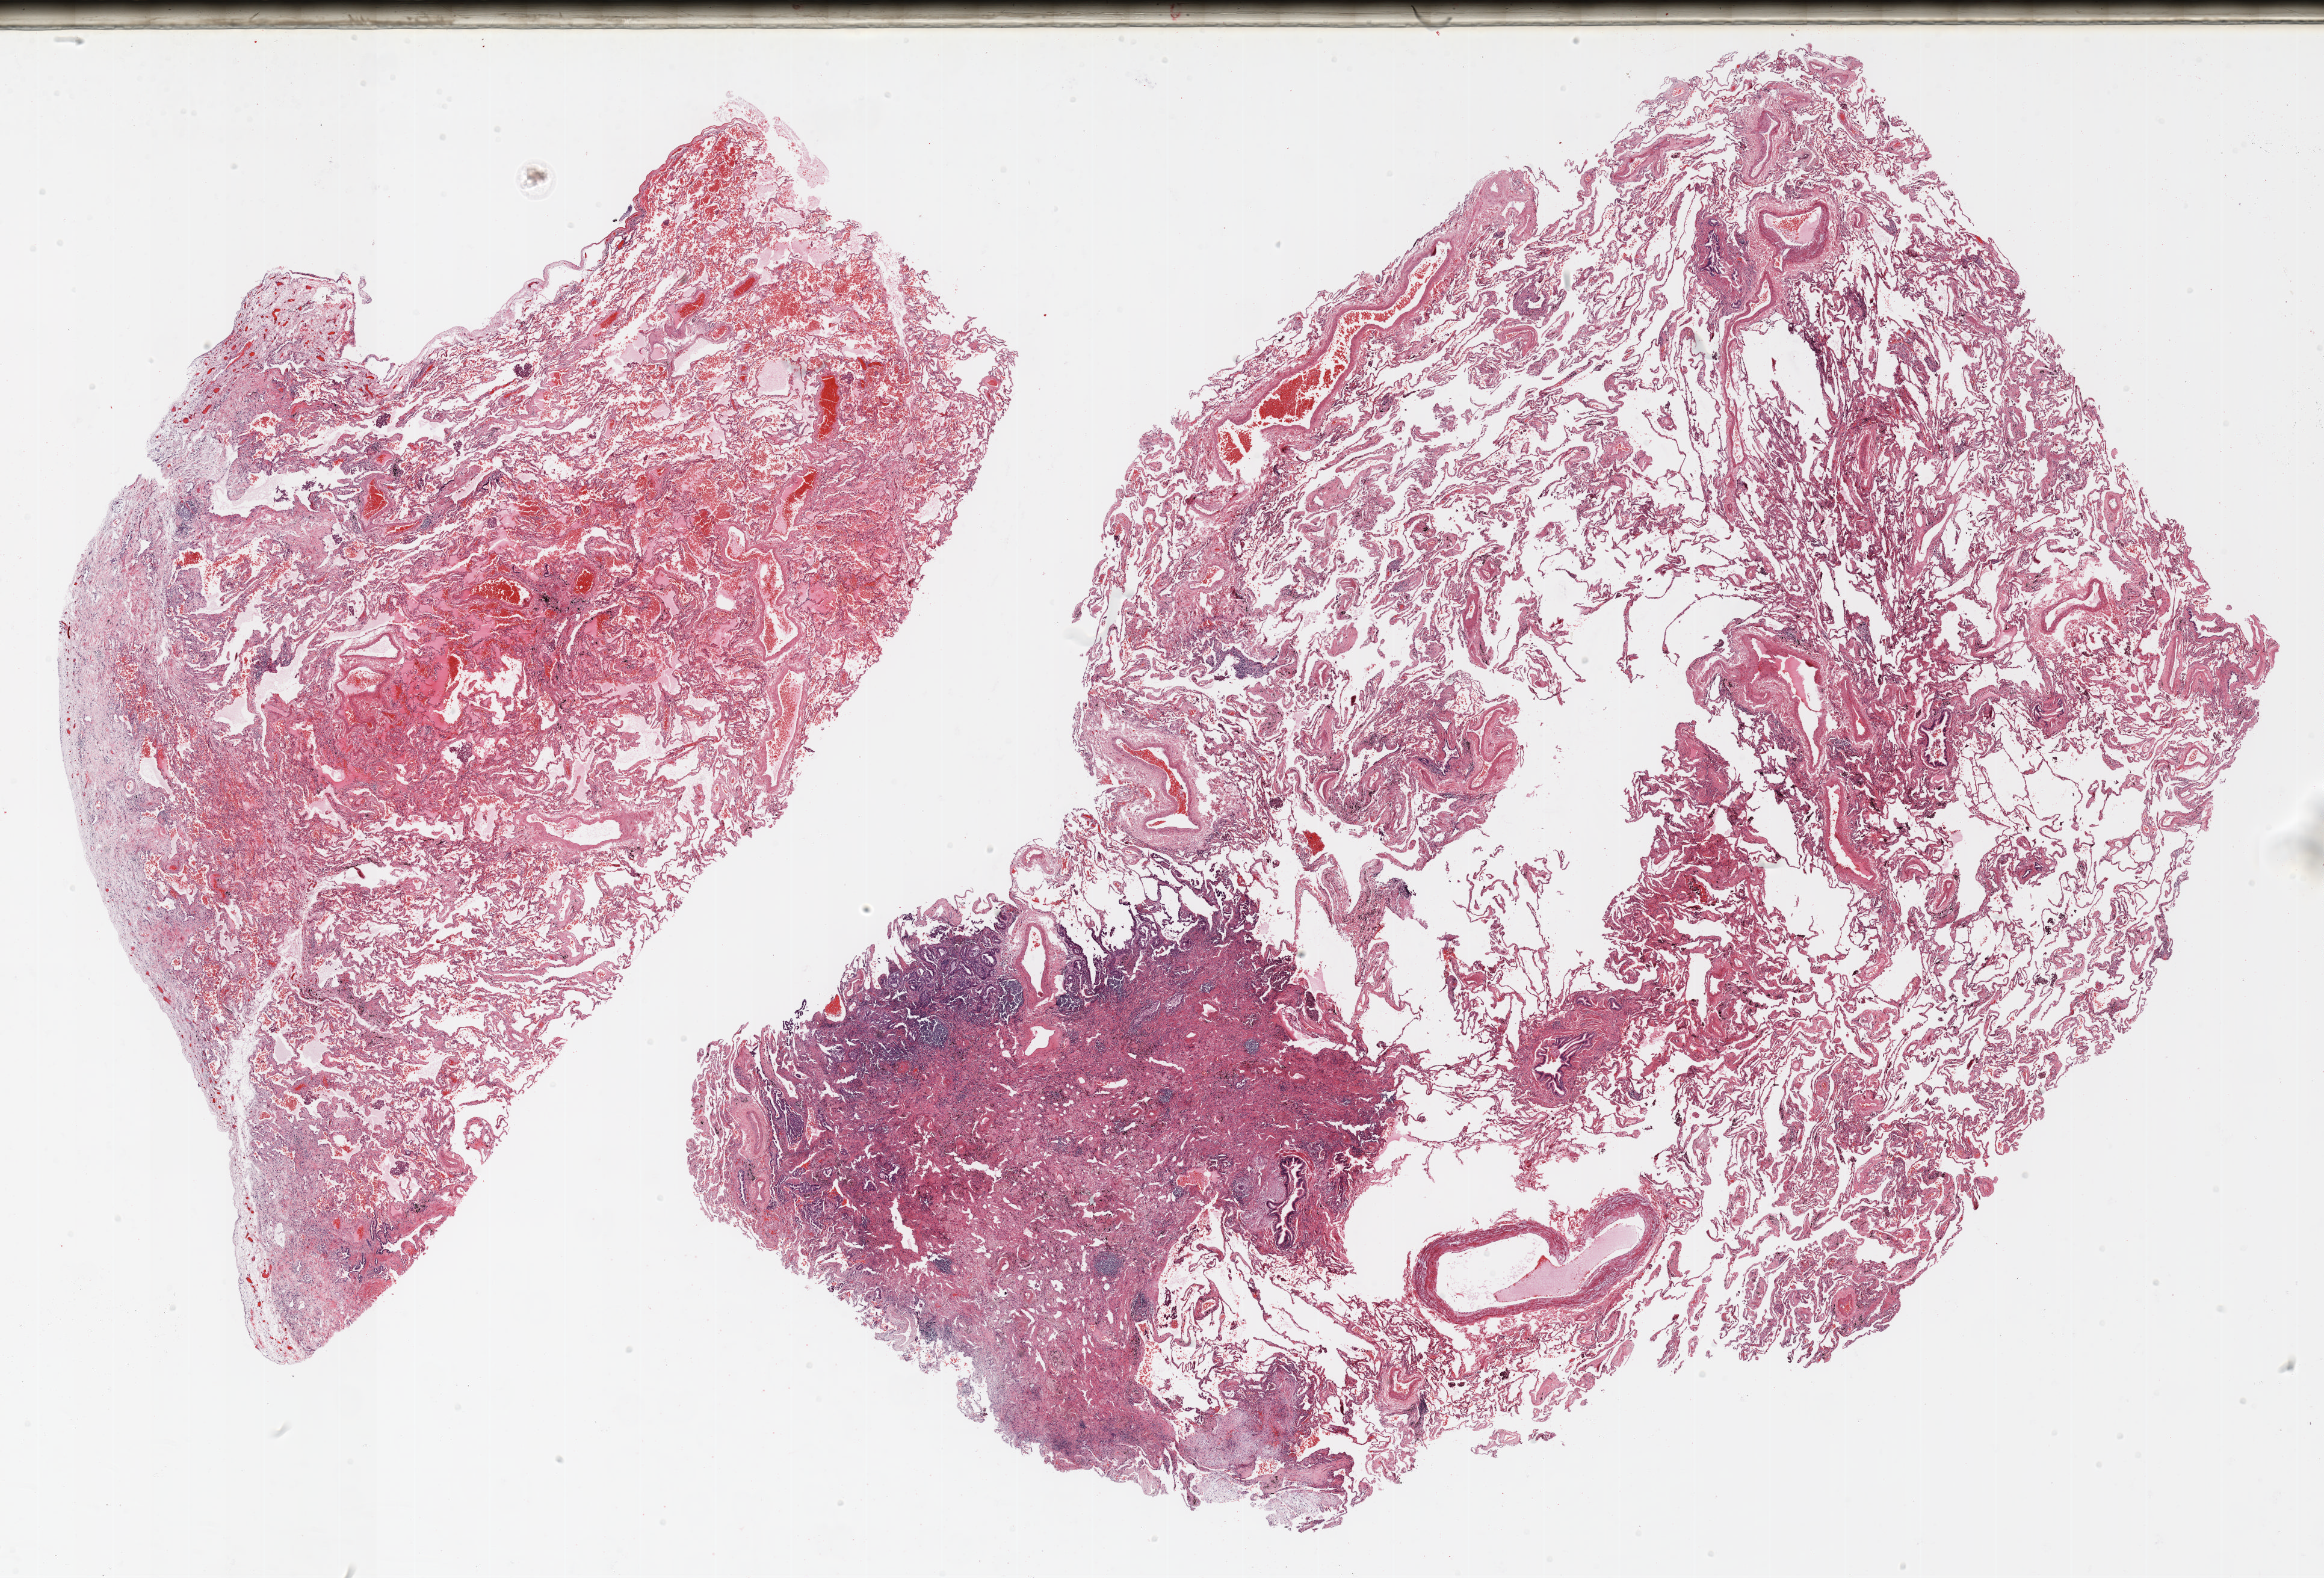
H&E-stained whole-slide image, shown as a low-resolution overview of the whole scanned area (about 31.0 x 21.1 mm, slide scanned at 20x). FFPE section. Lung. Female patient, aged 62 at enrolment.
Participant's lung-cancer diagnosis: Adenocarcinoma, NOS (ICD-O-3 8140/3).